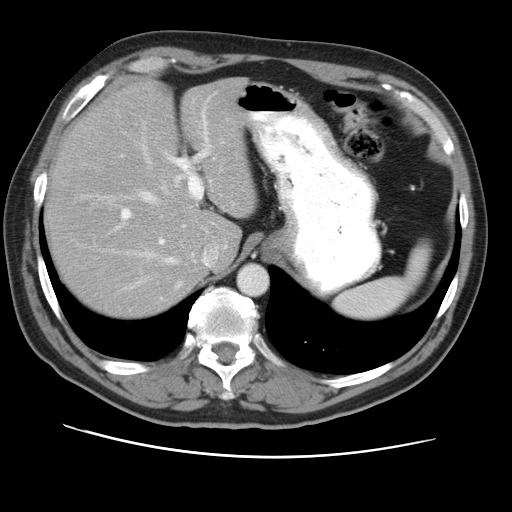
Contrast-enhanced abdominal CT, one axial slice. Position 36 of 49 along the scan axis. Reconstruction kernel STANDARD. 120 kVp. Soft-tissue window (W 400 / L 40 HU). 5 mm slice thickness. 512 × 512 image matrix, field of view 374 × 374 mm. Male patient, age 59 years. Case-level facts recorded for this patient, not image findings: diagnosis: colorectal cancer liver metastases, imaged before liver resection; multiple liver metastases: yes; largest metastasis: 6.3 cm; disease in both lobes: yes.
Structures marked on this image (expert manual segmentation):
- hepatic veins: bounding box <124,142,227,290> (left, top, right, bottom; pixels)
- liver: <48,79,255,316>
- planned liver remnant (the part of the liver to remain after resection): <48,79,255,316>
- portal vein (with intrahepatic branches): <121,131,210,245>